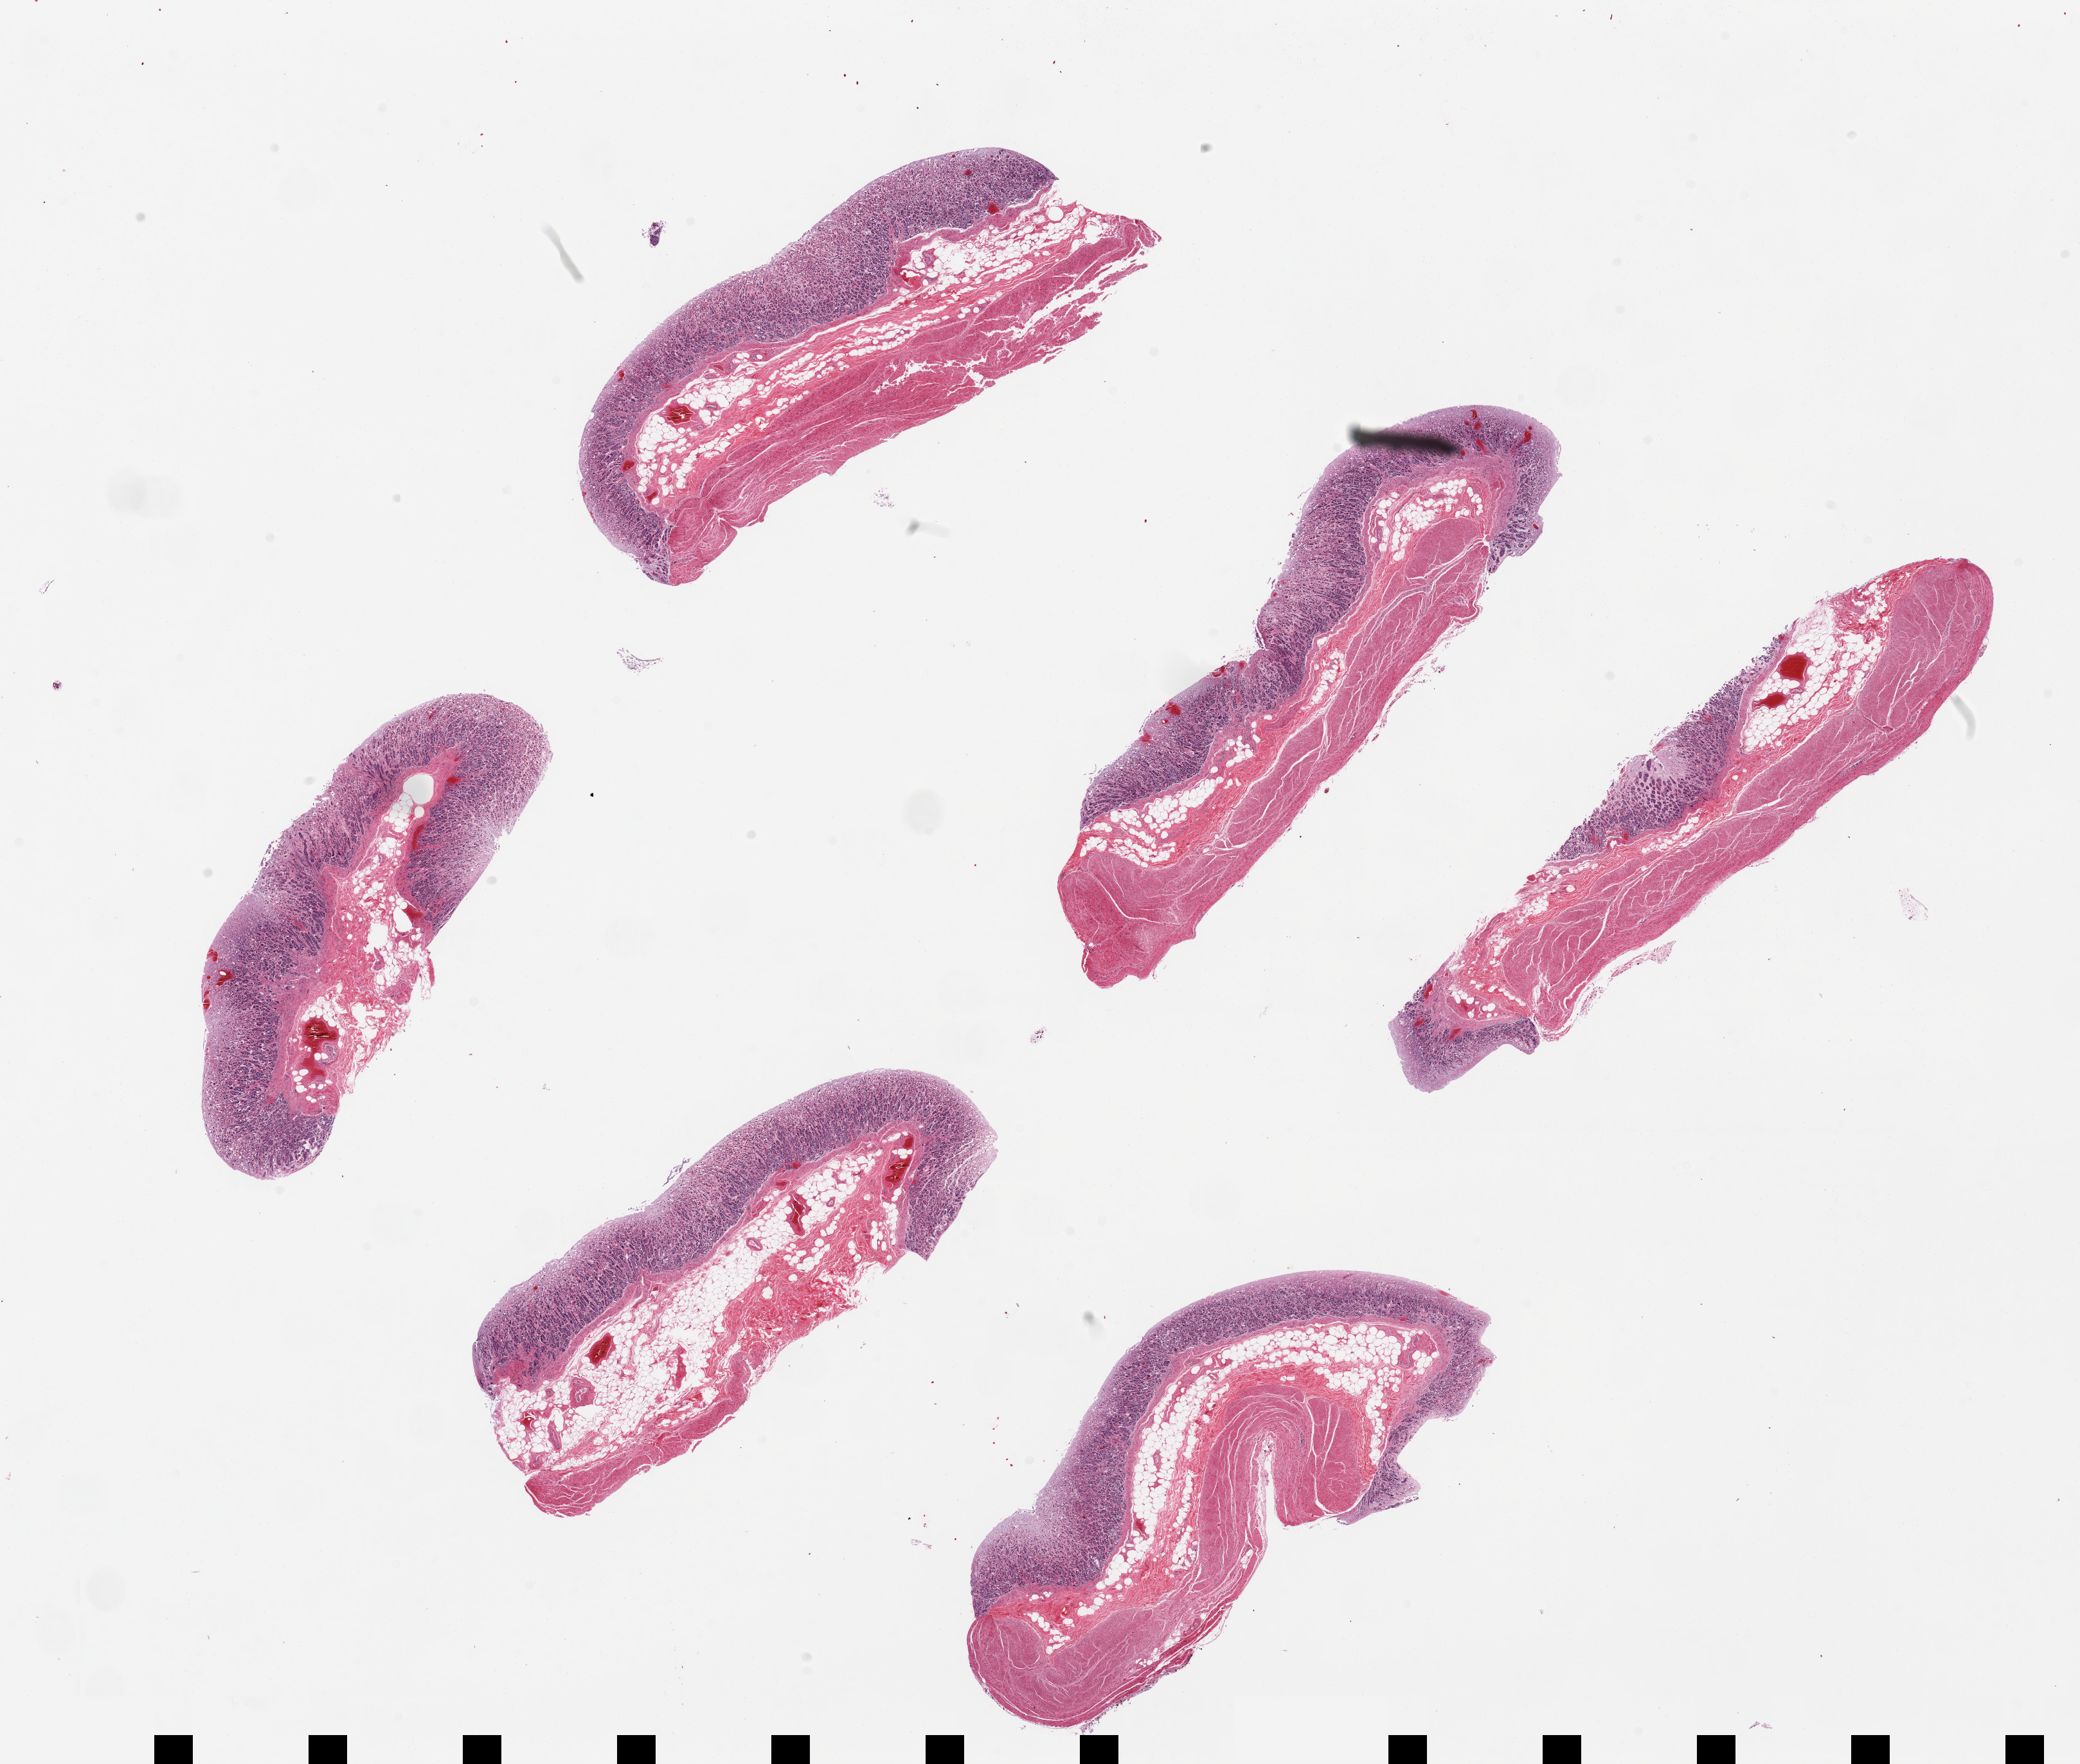
Whole-slide image, haematoxylin and eosin stain — whole scanned area (about 25.6 x 21.7 mm) shown as a low-resolution overview, PAXgene-fixed paraffin-embedded (PFPE) section, sampled site (target tissue): stomach, tissue donor sample. Donor: male.
Review note (as recorded): 6 pieces, mucosa is up to ~1mm thick, ~40-60% thickness but moderately-markedly autolyzed.